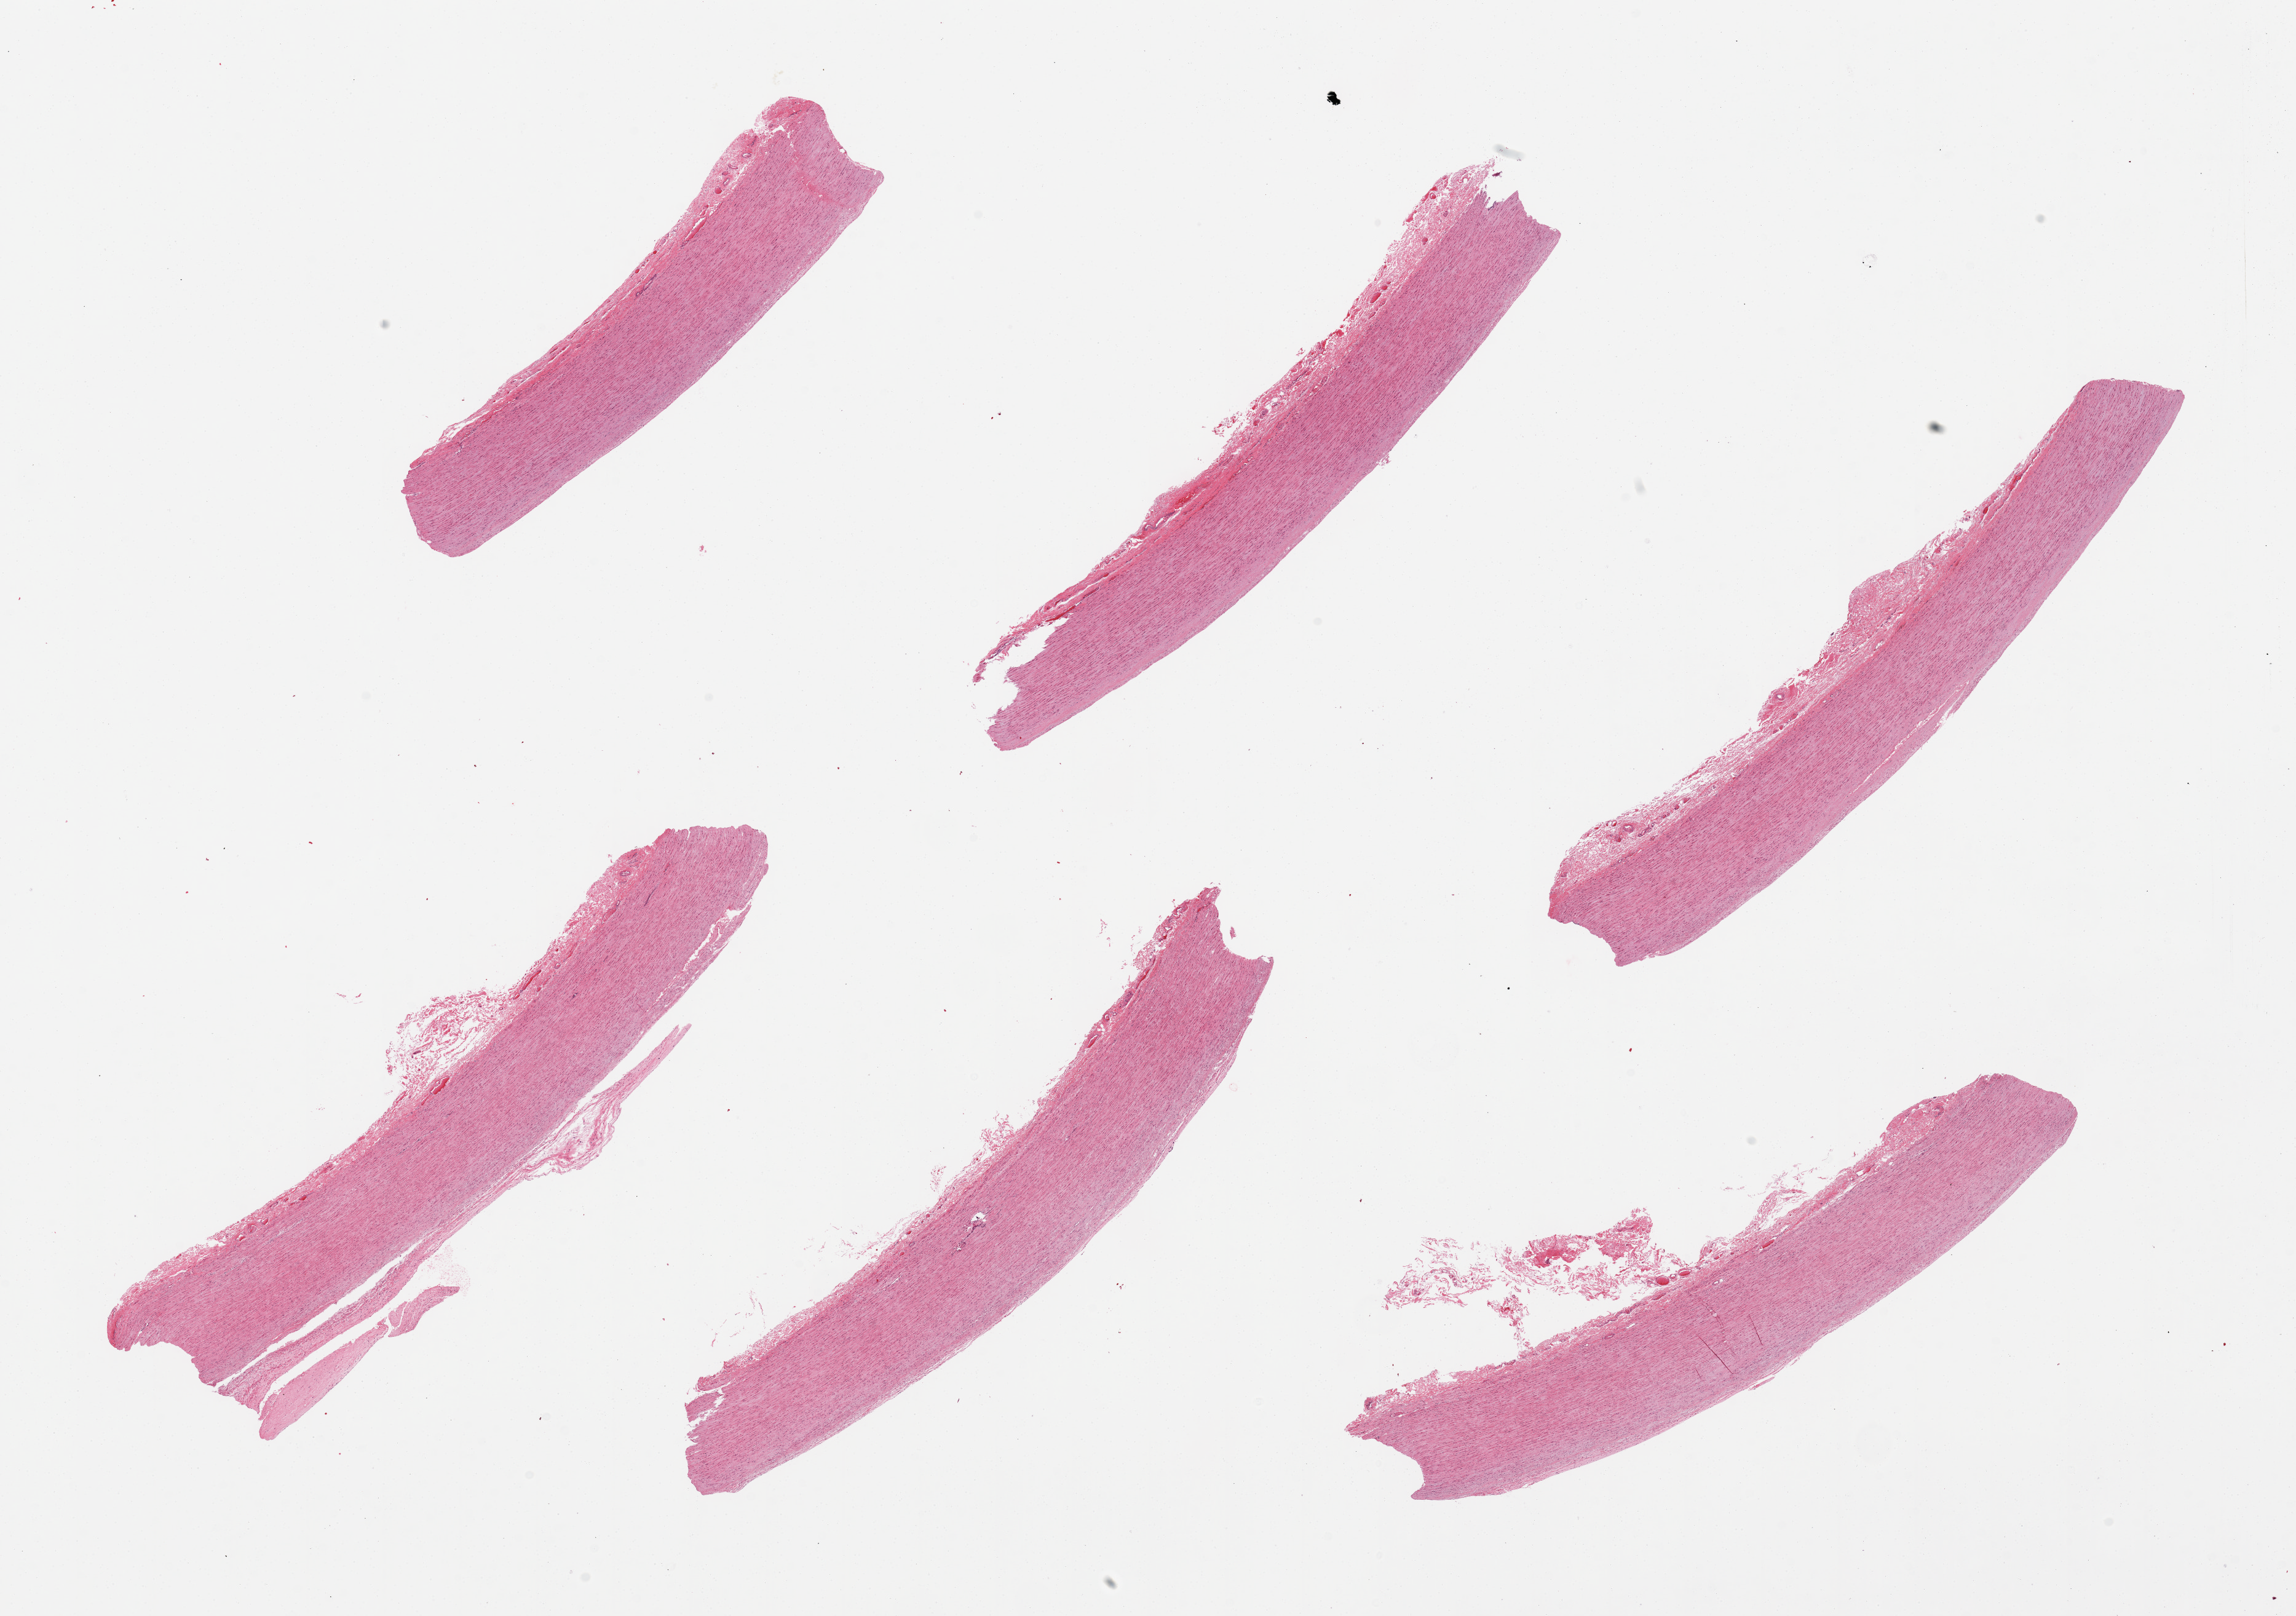
Hematoxylin and eosin (H&E) whole-slide image — a low-resolution overview of the entire scanned area, about 29.5 x 20.8 mm, PAXgene-fixed, paraffin-embedded tissue, target tissue: aorta, tissue donor sample. Female donor.
- review note (as recorded): 6 pieces; well trimmed